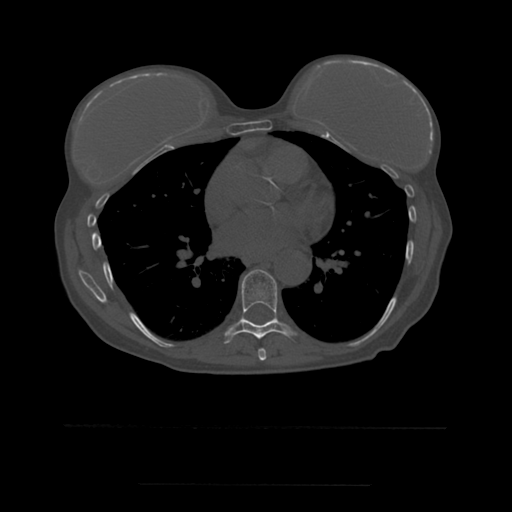
CT including the spine, one axial slice; slice 341 of 544 in the series (ordered by position); bone window (W 1800 / L 400 HU); 1.25 mm slice thickness; 512 × 512 image matrix. Patient age 58 years. From the clinical record (not read from this slice): primary cancer: lung.
Outlined on this slice (semi-automatic segmentation, software-assisted and operator-edited):
- T7 vertebra: box from (x=258, y=349) to (x=267, y=361) px
- T8 vertebra: (x=225, y=270)–(x=297, y=344)